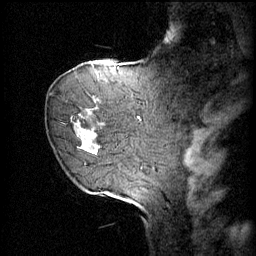
Breast MRI (dynamic contrast-enhanced), one sagittal slice; slice 14 of 60 in the series (ordered by position); 4 images stored at this slice position (order not interpretable as contrast timing); 1.5 T; TE 4.2 ms, TR 11 ms; 2 mm slice thickness; 256 × 256 image matrix. Female patient, age 72 years.
Outlined on this slice (semi-automatic segmentation, software-assisted and operator-edited):
- analysis volume of interest (the breast-tissue region the enhancement analysis was run in; not a lesion): bounding box [x1, y1, x2, y2] px = [68, 68, 109, 163]
- tumour enhancement mask (voxels above the 70 % enhancement threshold inside the analysis volume of interest): [71, 72, 107, 149]